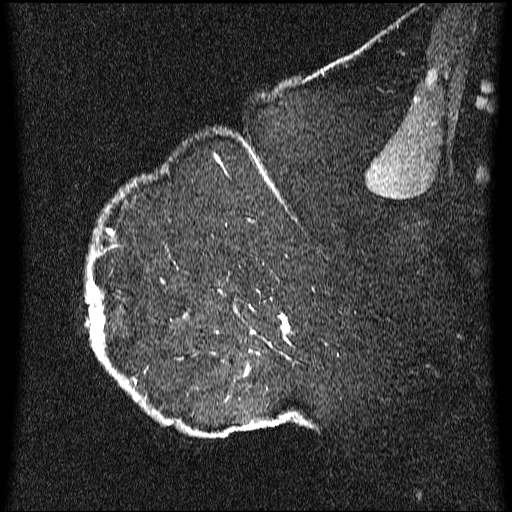
Breast MRI (dynamic contrast-enhanced), one sagittal slice; position 47 of 64 along the scan axis; dynamic contrast-enhanced series, image 2 of 3 at this slice position (ordered by acquisition); 1.5 T; TE 4.2 ms, TR 9.1 ms; 2.2 mm slice thickness; 512 × 512 image matrix, field of view 180 × 180 mm. Patient: female, 52 years.
Annotated regions visible in this slice (semi-automatically segmented with operator editing):
- analysis volume of interest (the breast-tissue region the enhancement analysis was run in; not a lesion): bounding box <86,203,337,438> (left, top, right, bottom; pixels)
- tumour enhancement mask (voxels above the 70 % enhancement threshold inside the analysis volume of interest): <88,231,298,437>